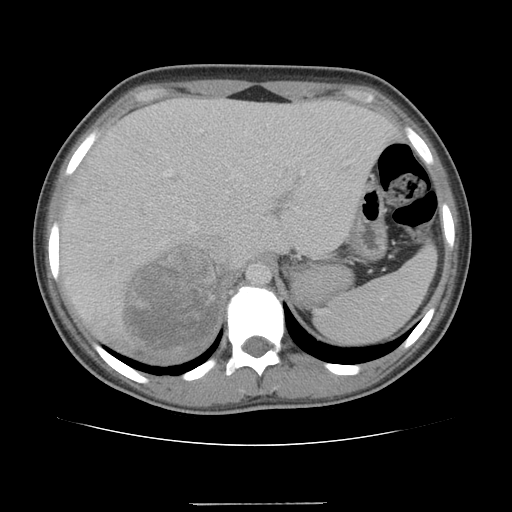
Contrast-enhanced abdominal CT, one axial slice; position 80 of 100 along the scan axis; 120 kVp; intravenous contrast given; soft-tissue window (W 400 / L 40 HU); 5 mm slice thickness; 512 × 512 image matrix, field of view 360 × 360 mm. Patient: female, 21 years. From the clinical record (not read from this slice): diagnosis: adrenocortical carcinoma; tumour side: right adrenal; tumour size at pathology: 15.5 cm; Ki-67 index: 26 %; stage (as recorded): 3.
Outlined on this slice (semi-automatically segmented with operator editing):
- mass: box from (x=125, y=252) to (x=217, y=348) px